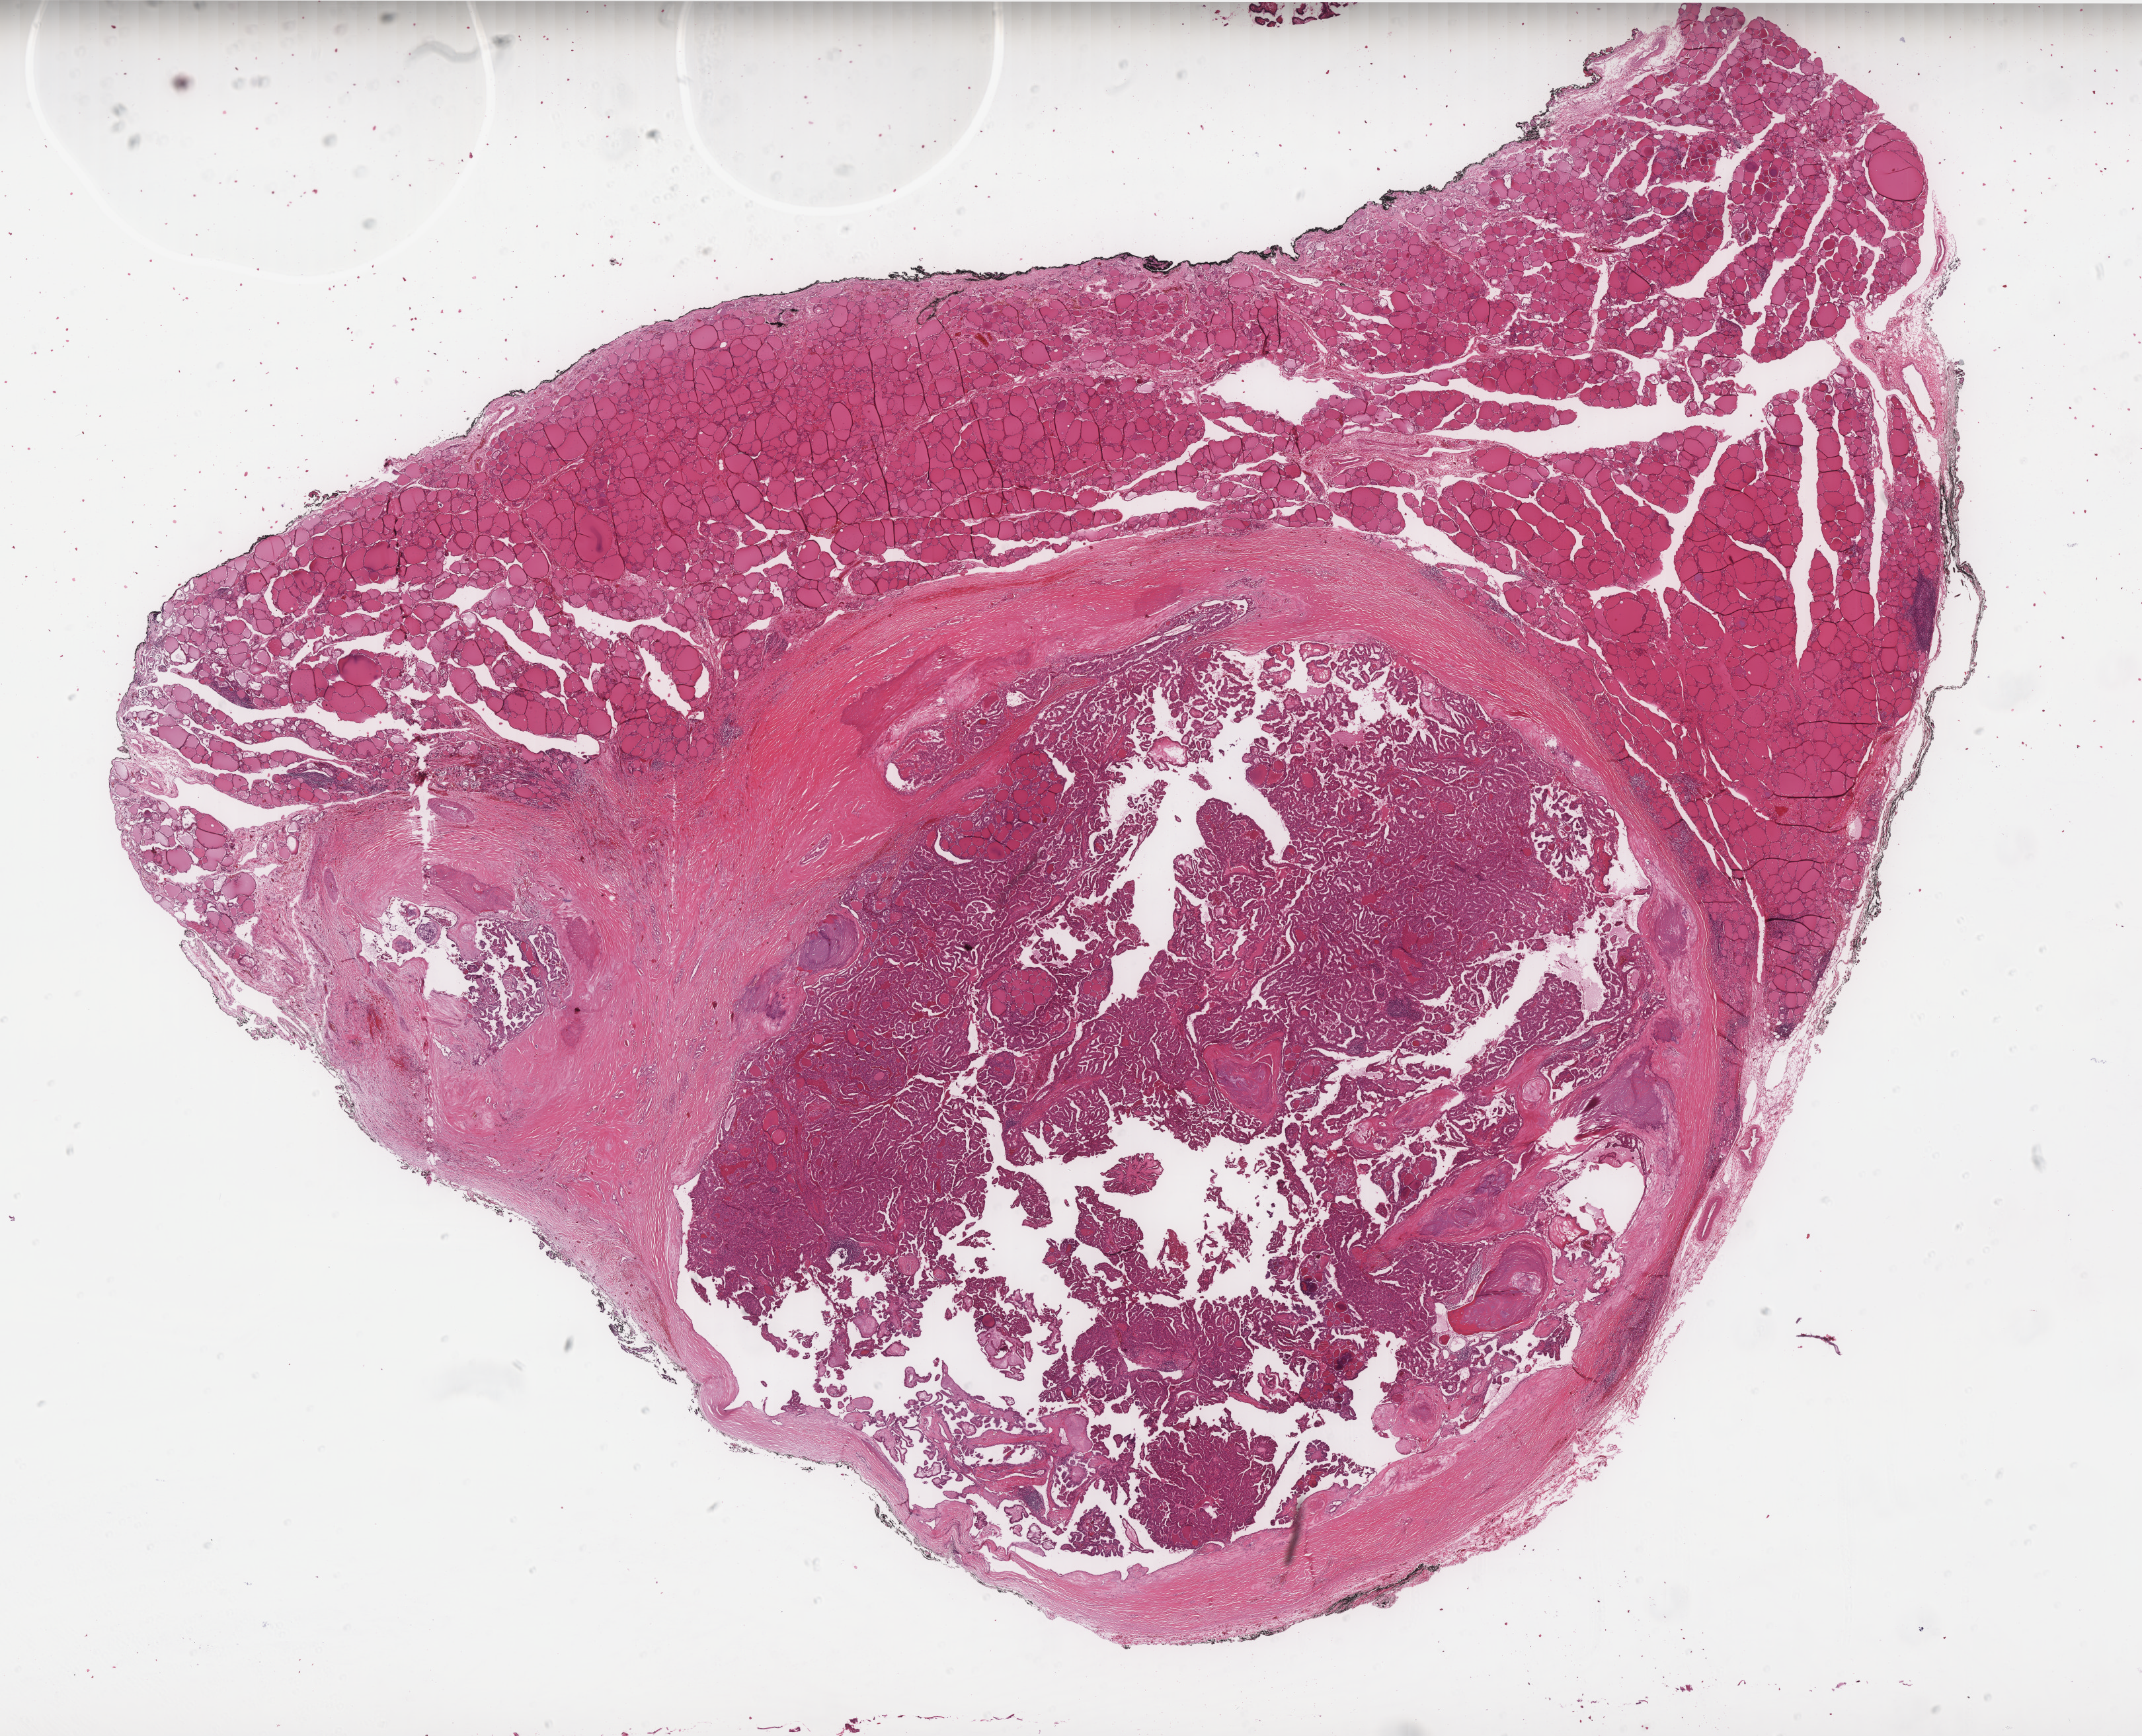
Whole-slide histology image, H&E-stained — shown as a low-resolution overview of the whole scanned area (about 26.0 x 21.1 mm, acquisition: 40x scan); FFPE section; thyroid, primary tumour sample. Female, age 52 years at initial diagnosis.
Pathologic diagnosis: Papillary carcinoma, columnar cell (thyroid gland). AJCC pathologic stage: IVA (7th edition). Lymph nodes positive (case pathology): 1 of 4 examined. Laterality: bilateral.